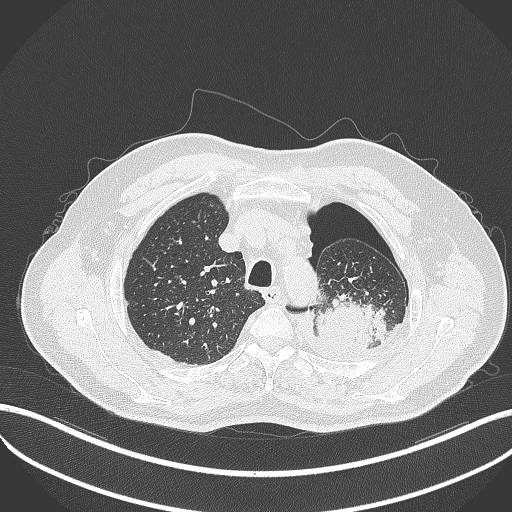
Chest CT, one axial slice; position 405 of 464 along the scan axis; lung window (W 1500 / L -600 HU); 1 mm slice thickness; 512 × 512 image matrix, field of view 400 × 400 mm. Patient: male, 76 years. Case-level facts recorded for this patient, not image findings: clinical TNM (as recorded): T3 N0 M1b.
Structures marked on this image (rectangle marked by the reading radiologist):
- lung tumour (recorded histology: adenocarcinoma): box from (x=311, y=296) to (x=387, y=354) px